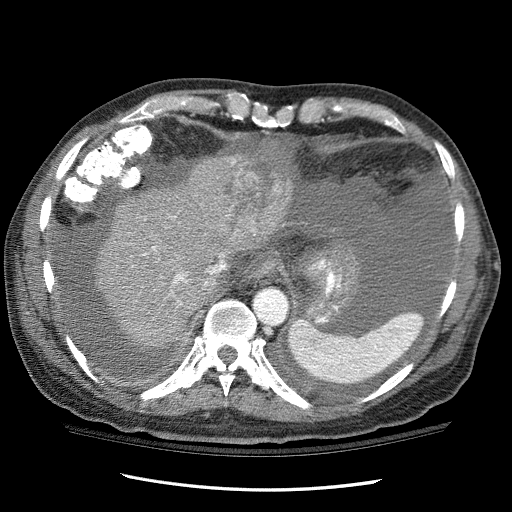
Contrast-enhanced abdominal CT (liver protocol), one axial slice; position 90 of 114 along the scan axis; 120 kVp; one of 3 acquisitions stored at this slice position; soft-tissue window (W 400 / L 40 HU); 512 × 512 image matrix. From the clinical record (not read from this slice): diagnosis: hepatocellular carcinoma (patient treated with transarterial chemoembolisation; whether this scan precedes or follows treatment is not stated here); TNM stage (as recorded): Stage-I; Child-Pugh class: C; tumour nodularity: uninodular.
Outlined on this slice (semi-automatically segmented with operator editing):
- liver parenchyma outside the tumour (the mass and vessels are separate outlines, so this box may not span the whole liver): bounding box (x1, y1, x2, y2) in pixels: (95, 147, 282, 348)
- mass: (186, 155, 296, 238)
- liver vessels: (143, 246, 223, 284)